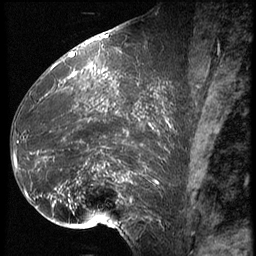
Breast MRI (dynamic contrast-enhanced), one sagittal slice; position 29 of 62 along the scan axis; 3 images stored at this slice position (order not interpretable as contrast timing); 1.5 T; TE 4.2 ms, TR 9 ms; 2.5 mm slice thickness; 256 × 256 image matrix, field of view 180 × 180 mm. Patient: female, 39 years. From the clinical record (not read from this slice): setting: breast cancer imaged before/during neoadjuvant chemotherapy; receptor status: HER2-positive.
Outlined on this slice (semi-automatic segmentation, software-assisted and operator-edited):
- analysis volume of interest (the breast-tissue region the enhancement analysis was run in; not a lesion): box from (x=16, y=64) to (x=171, y=228) px
- tumour enhancement mask (voxels above the 140 % enhancement threshold inside the analysis volume of interest): (x=16, y=70)–(x=171, y=224)